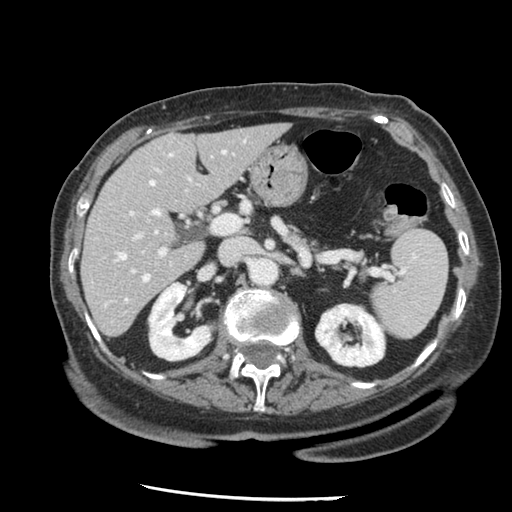
Contrast-enhanced abdominal CT, one axial slice; slice 74 of 148 in the series (ordered by position); soft-tissue window (W 400 / L 40 HU); 2.5 mm slice thickness; 512 × 512 image matrix, field of view 330 × 330 mm. Female patient, age 85 years. From the clinical record (not read from this slice): diagnosis: colorectal cancer liver metastases, imaged before liver resection; multiple liver metastases: no; largest metastasis: 0.9 cm; disease in both lobes: no.
Outlined on this slice (manually delineated by an expert):
- hepatic veins: bounding box [x1, y1, x2, y2] px = [118, 152, 175, 301]
- liver: [83, 125, 287, 336]
- planned liver remnant (the part of the liver to remain after resection): [83, 125, 287, 336]
- portal vein (with intrahepatic branches): [130, 149, 229, 273]